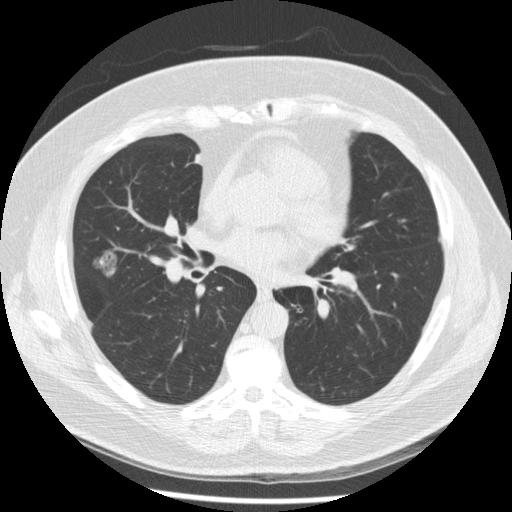
Axial slice from a low-dose chest CT screening exam; second annual screen; lung window (W 1500 / L -600 HU); 2.5 mm slice thickness; 120 kVp; slice 118 of 230 in the series; 512 × 512 image matrix, field of view 360 × 360 mm. Male participant, aged 67 years at enrolment. Former smoker at enrolment.
Lesion marked by an expert reader, bounding box [x1, y1, x2, y2] px = [80, 244, 124, 287]. The exam's reader record, not a measurement of the box and not confirmed to be the same lesion: non-calcified nodule or mass ≥4 mm, right middle lobe, 19 × 16 mm, smooth margins, soft tissue attenuation, pre-existing on the prior screen: yes; interval growth: yes. Later outcome: lung cancer diagnosed 47 days after this screen — adenocarcinoma, NOS, right middle lobe, moderately differentiated (G2), stage IA (AJCC 6th edition), 14 mm at pathology.